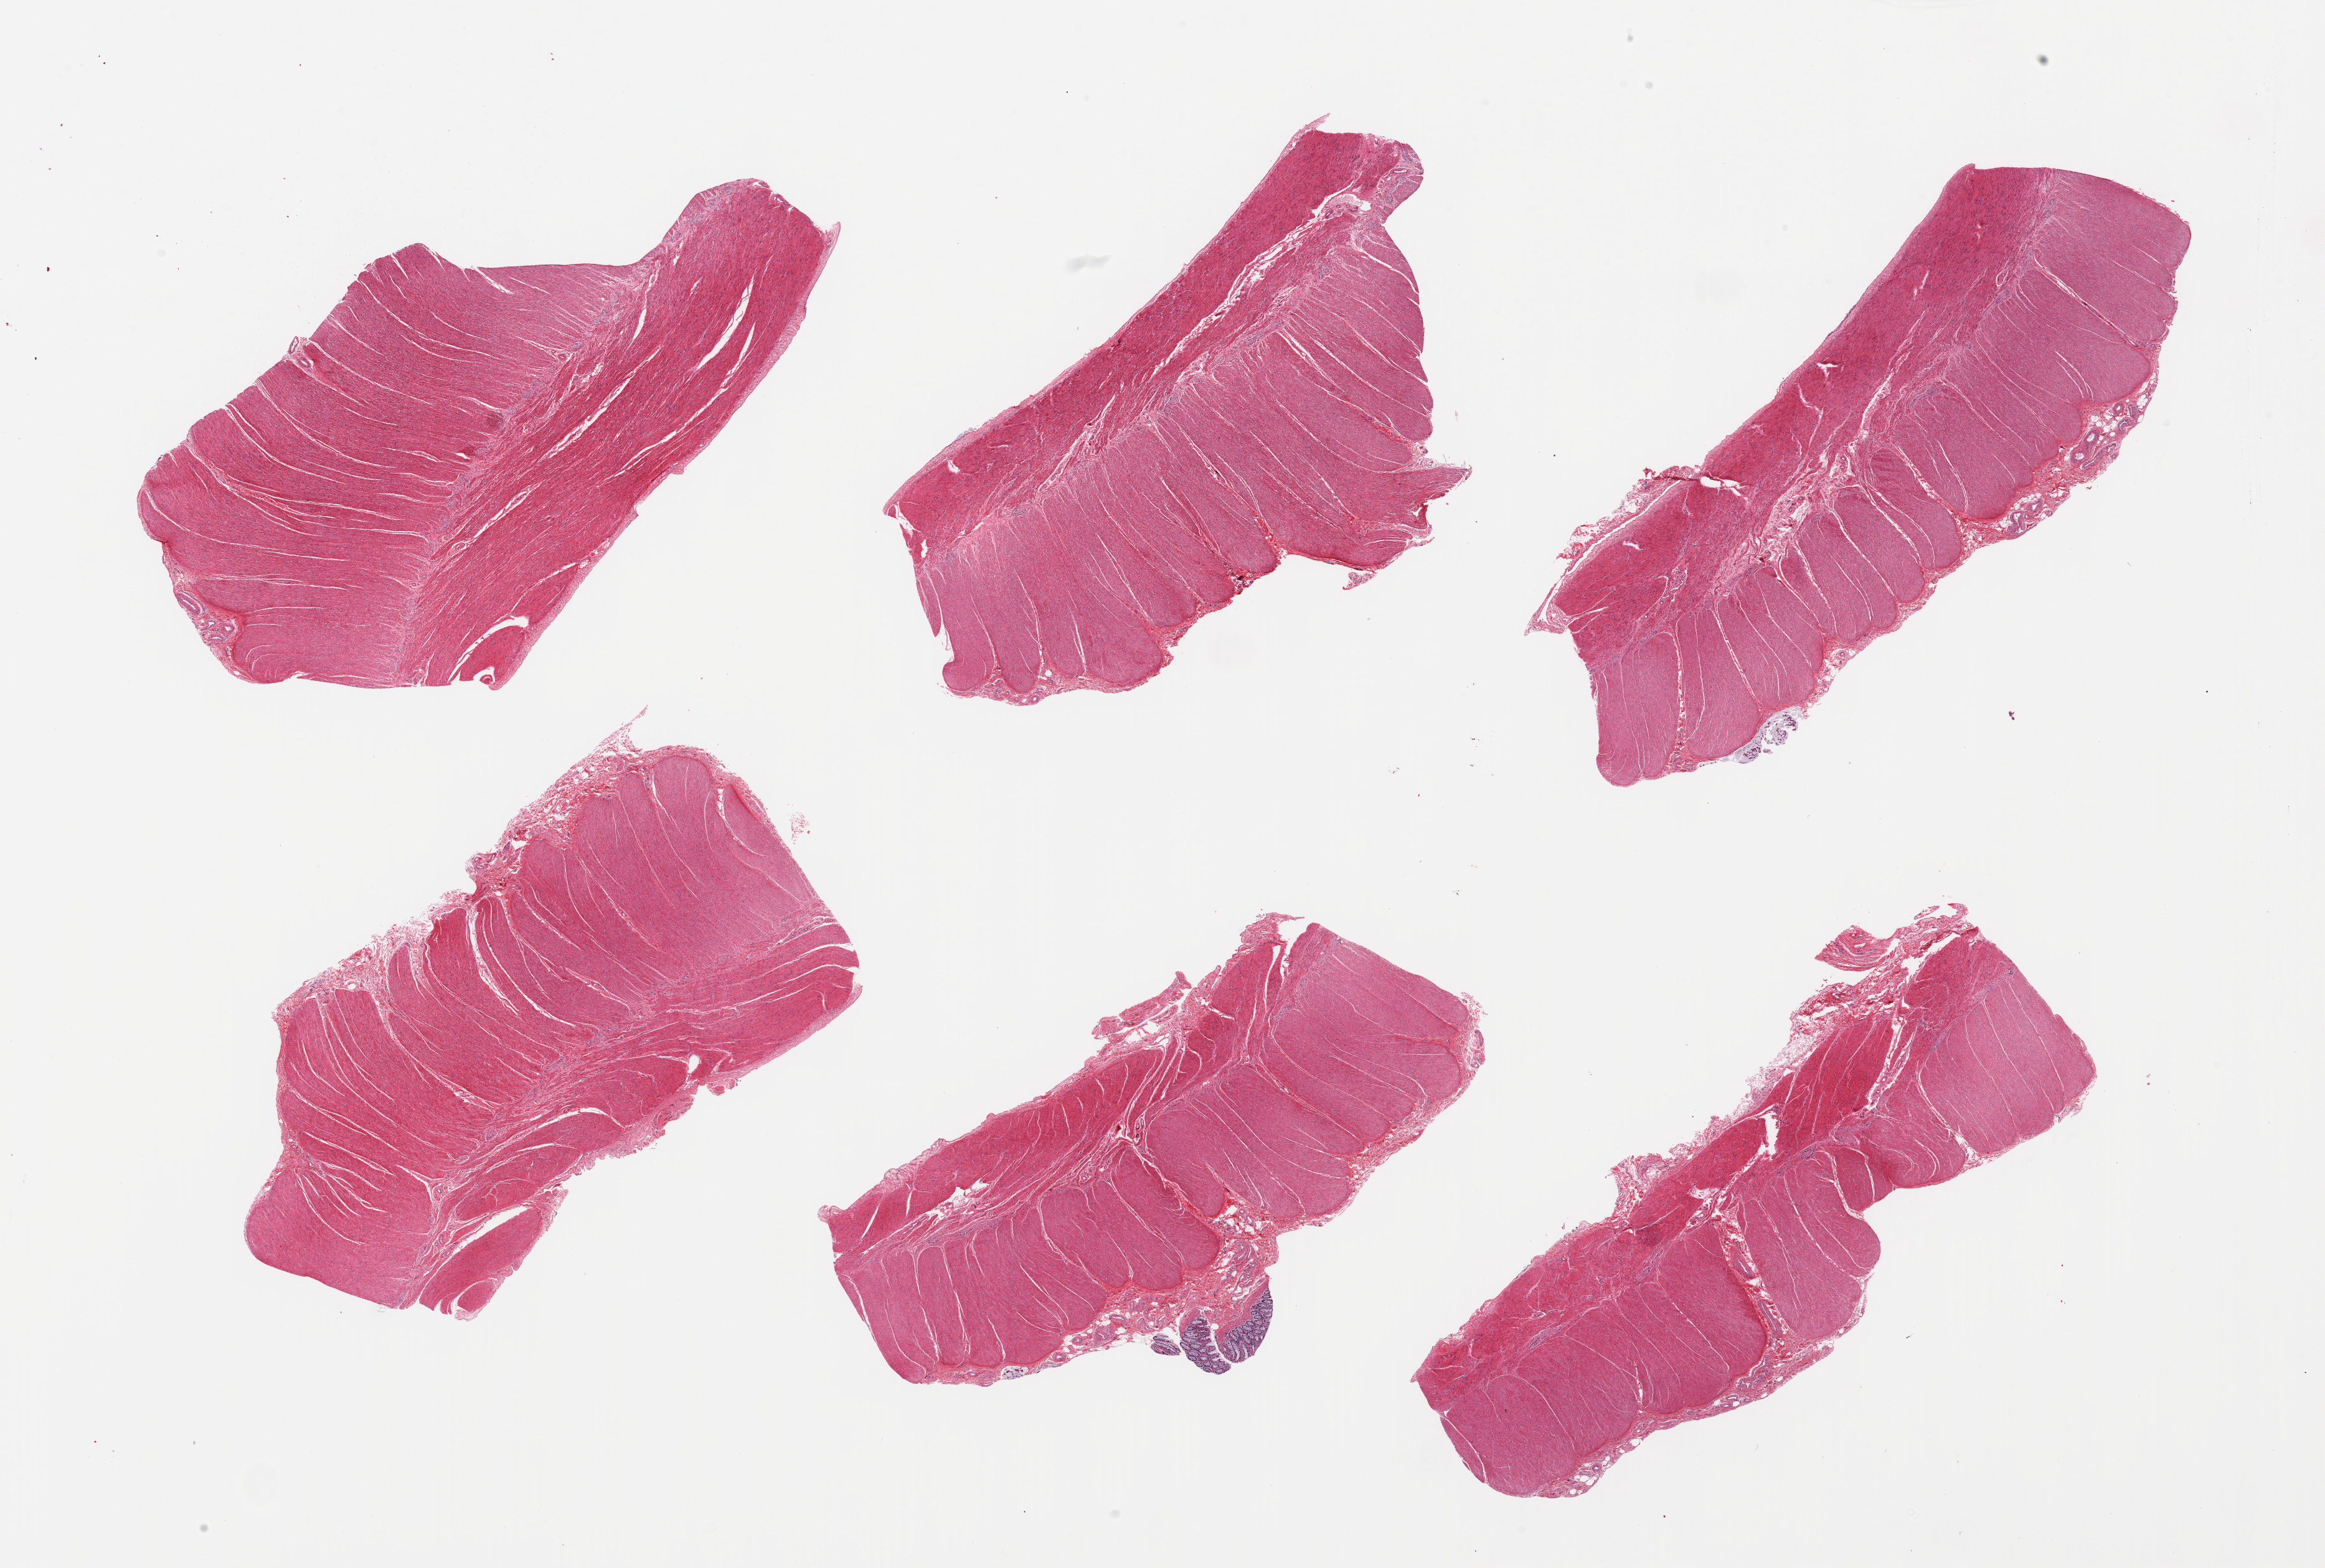
Digitized hematoxylin and eosin (H&E)-stained section — low-resolution overview of the scanned area, about 29.5 x 19.9 mm, PAXgene-fixed, paraffin-embedded tissue, sampled site (target tissue): sigmoid colon, tissue donor sample. Donor: female.
Reviewer comment on this tissue sample: 6 pieces; 1.2 mm nubbin of mucosa on 1 piece.